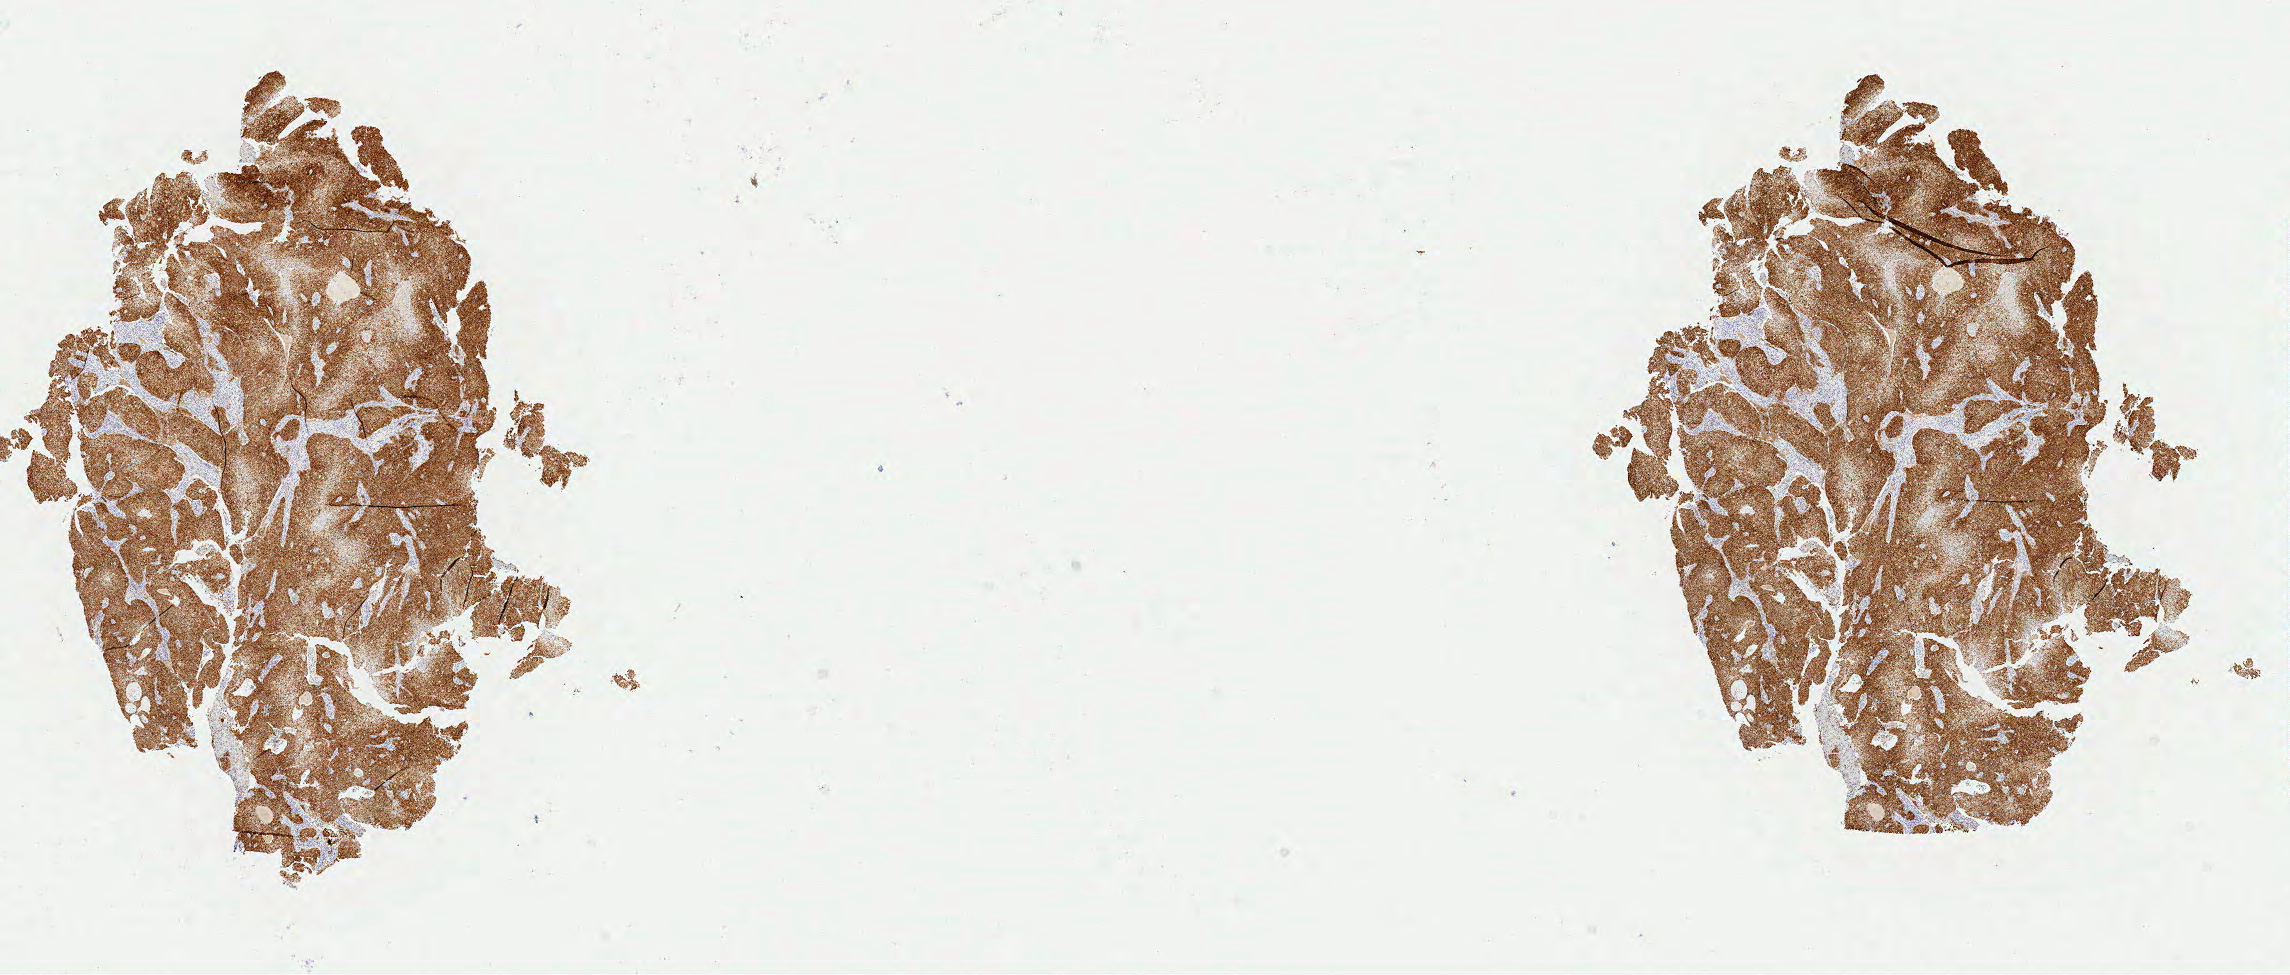
Whole-slide image, immunohistochemical stain for p16 (p16INK4a), whole scanned area (about 18.1 x 7.7 mm) shown as a low-resolution overview; specimen: tumor tissue; anatomic site: cervix. Patient female; 39 years old.
Diagnosis: Squamous cell carcinoma, large cell, nonkeratinizing, NOS.